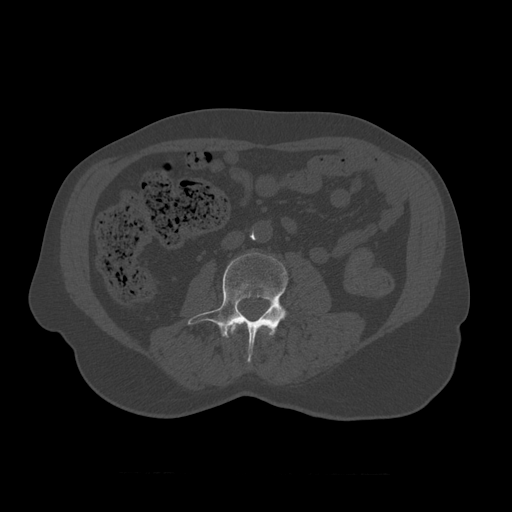
CT including the spine, one axial slice. Slice 304 of 450 in the series (ordered by position). Reconstruction kernel STANDARD. Bone window (W 1800 / L 400 HU). 1.25 mm slice thickness. 512 × 512 image matrix, field of view 405 × 405 mm. Patient age 75 years. From the clinical record (not read from this slice): primary cancer: prostate.
Structures marked on this image (semi-automatic segmentation, software-assisted and operator-edited):
- L2 vertebra: bounding box [x1, y1, x2, y2] px = [231, 322, 271, 337]
- L3 vertebra: [188, 253, 288, 363]